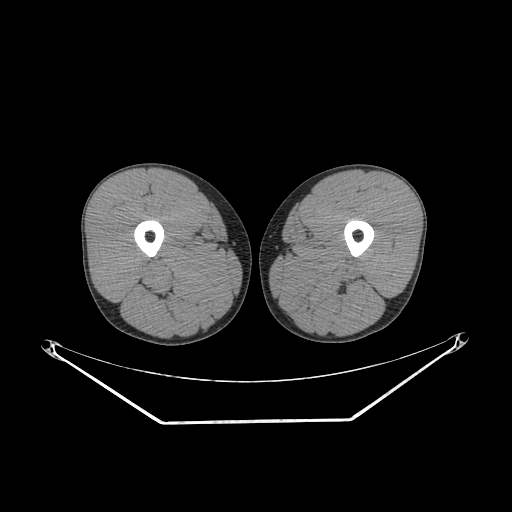
CT of an extremity soft-tissue mass (from a PET/CT study), one axial slice. Slice 227 of 267 in the series (ordered by position). Reconstruction kernel SOFT. Soft-tissue window (W 400 / L 40 HU). 3.75 mm slice thickness. 512 × 512 image matrix. Male patient. From the clinical record (not read from this slice): histological type: extraskeletal osteosarcoma; grade: high; site of the primary tumour: left adductur.
Outlined on this slice (expert contour drawn on MRI and transferred to this co-registered scan by the dataset authors):
- gross tumour volume (mass): bounding box [x1, y1, x2, y2] px = [274, 247, 369, 307]